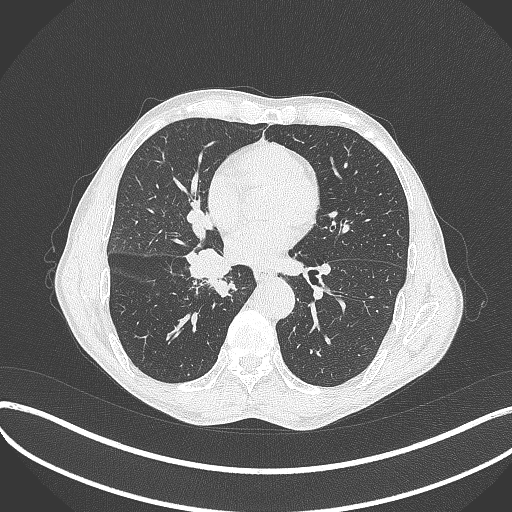
Chest CT, one axial slice. Position 200 of 481 along the scan axis. 120 kVp. Lung window (W 1500 / L -600 HU). 1 mm slice thickness. 512 × 512 image matrix, field of view 400 × 400 mm. Male patient, age 65 years. From the clinical record (not read from this slice): clinical TNM (as recorded): T2a N0 M0.
Annotated regions visible in this slice (bounding box drawn by a radiologist):
- lung tumour (recorded histology: squamous cell carcinoma): bounding box (x1, y1, x2, y2) in pixels: (176, 240, 244, 306)